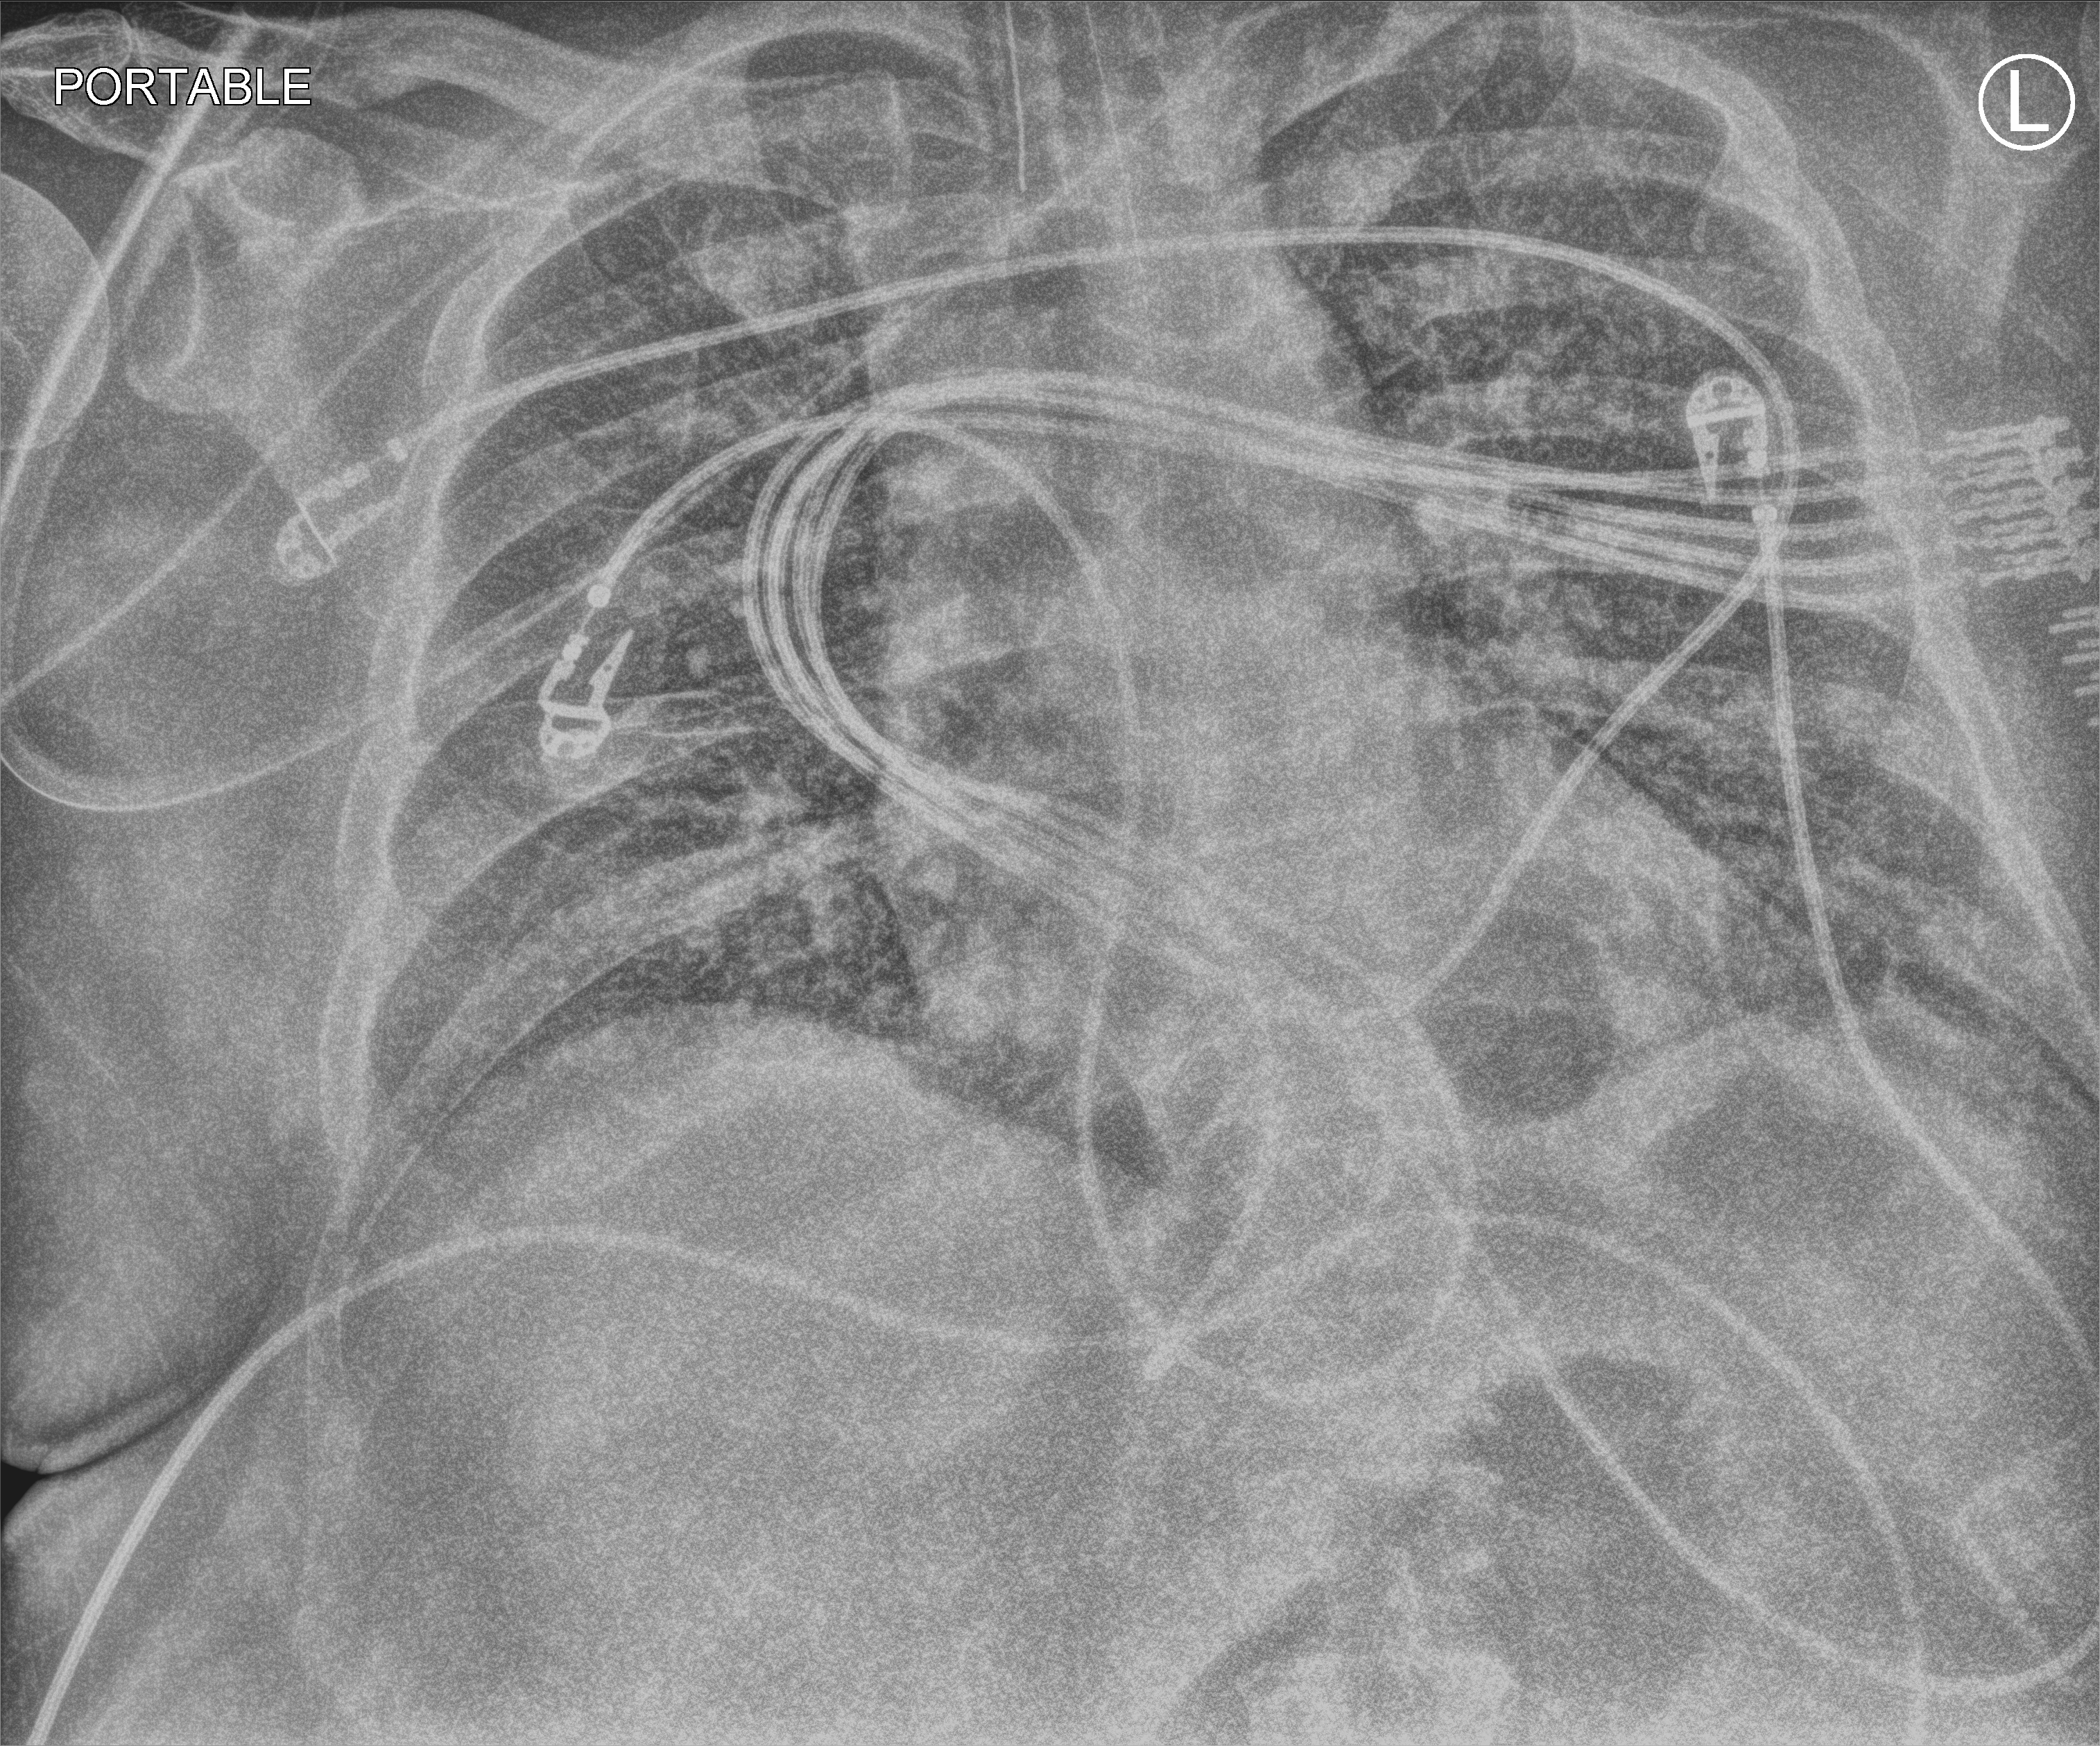
Portable chest radiograph. Adult patient hospitalised with COVID-19, age 18–59 years.
Admission-level facts for this patient (not findings on this image; timing relative to this image not recorded):
- mechanically ventilated during this hospital stay: yes
- chronic kidney disease (admission record): no
- length of hospital stay: 26 days